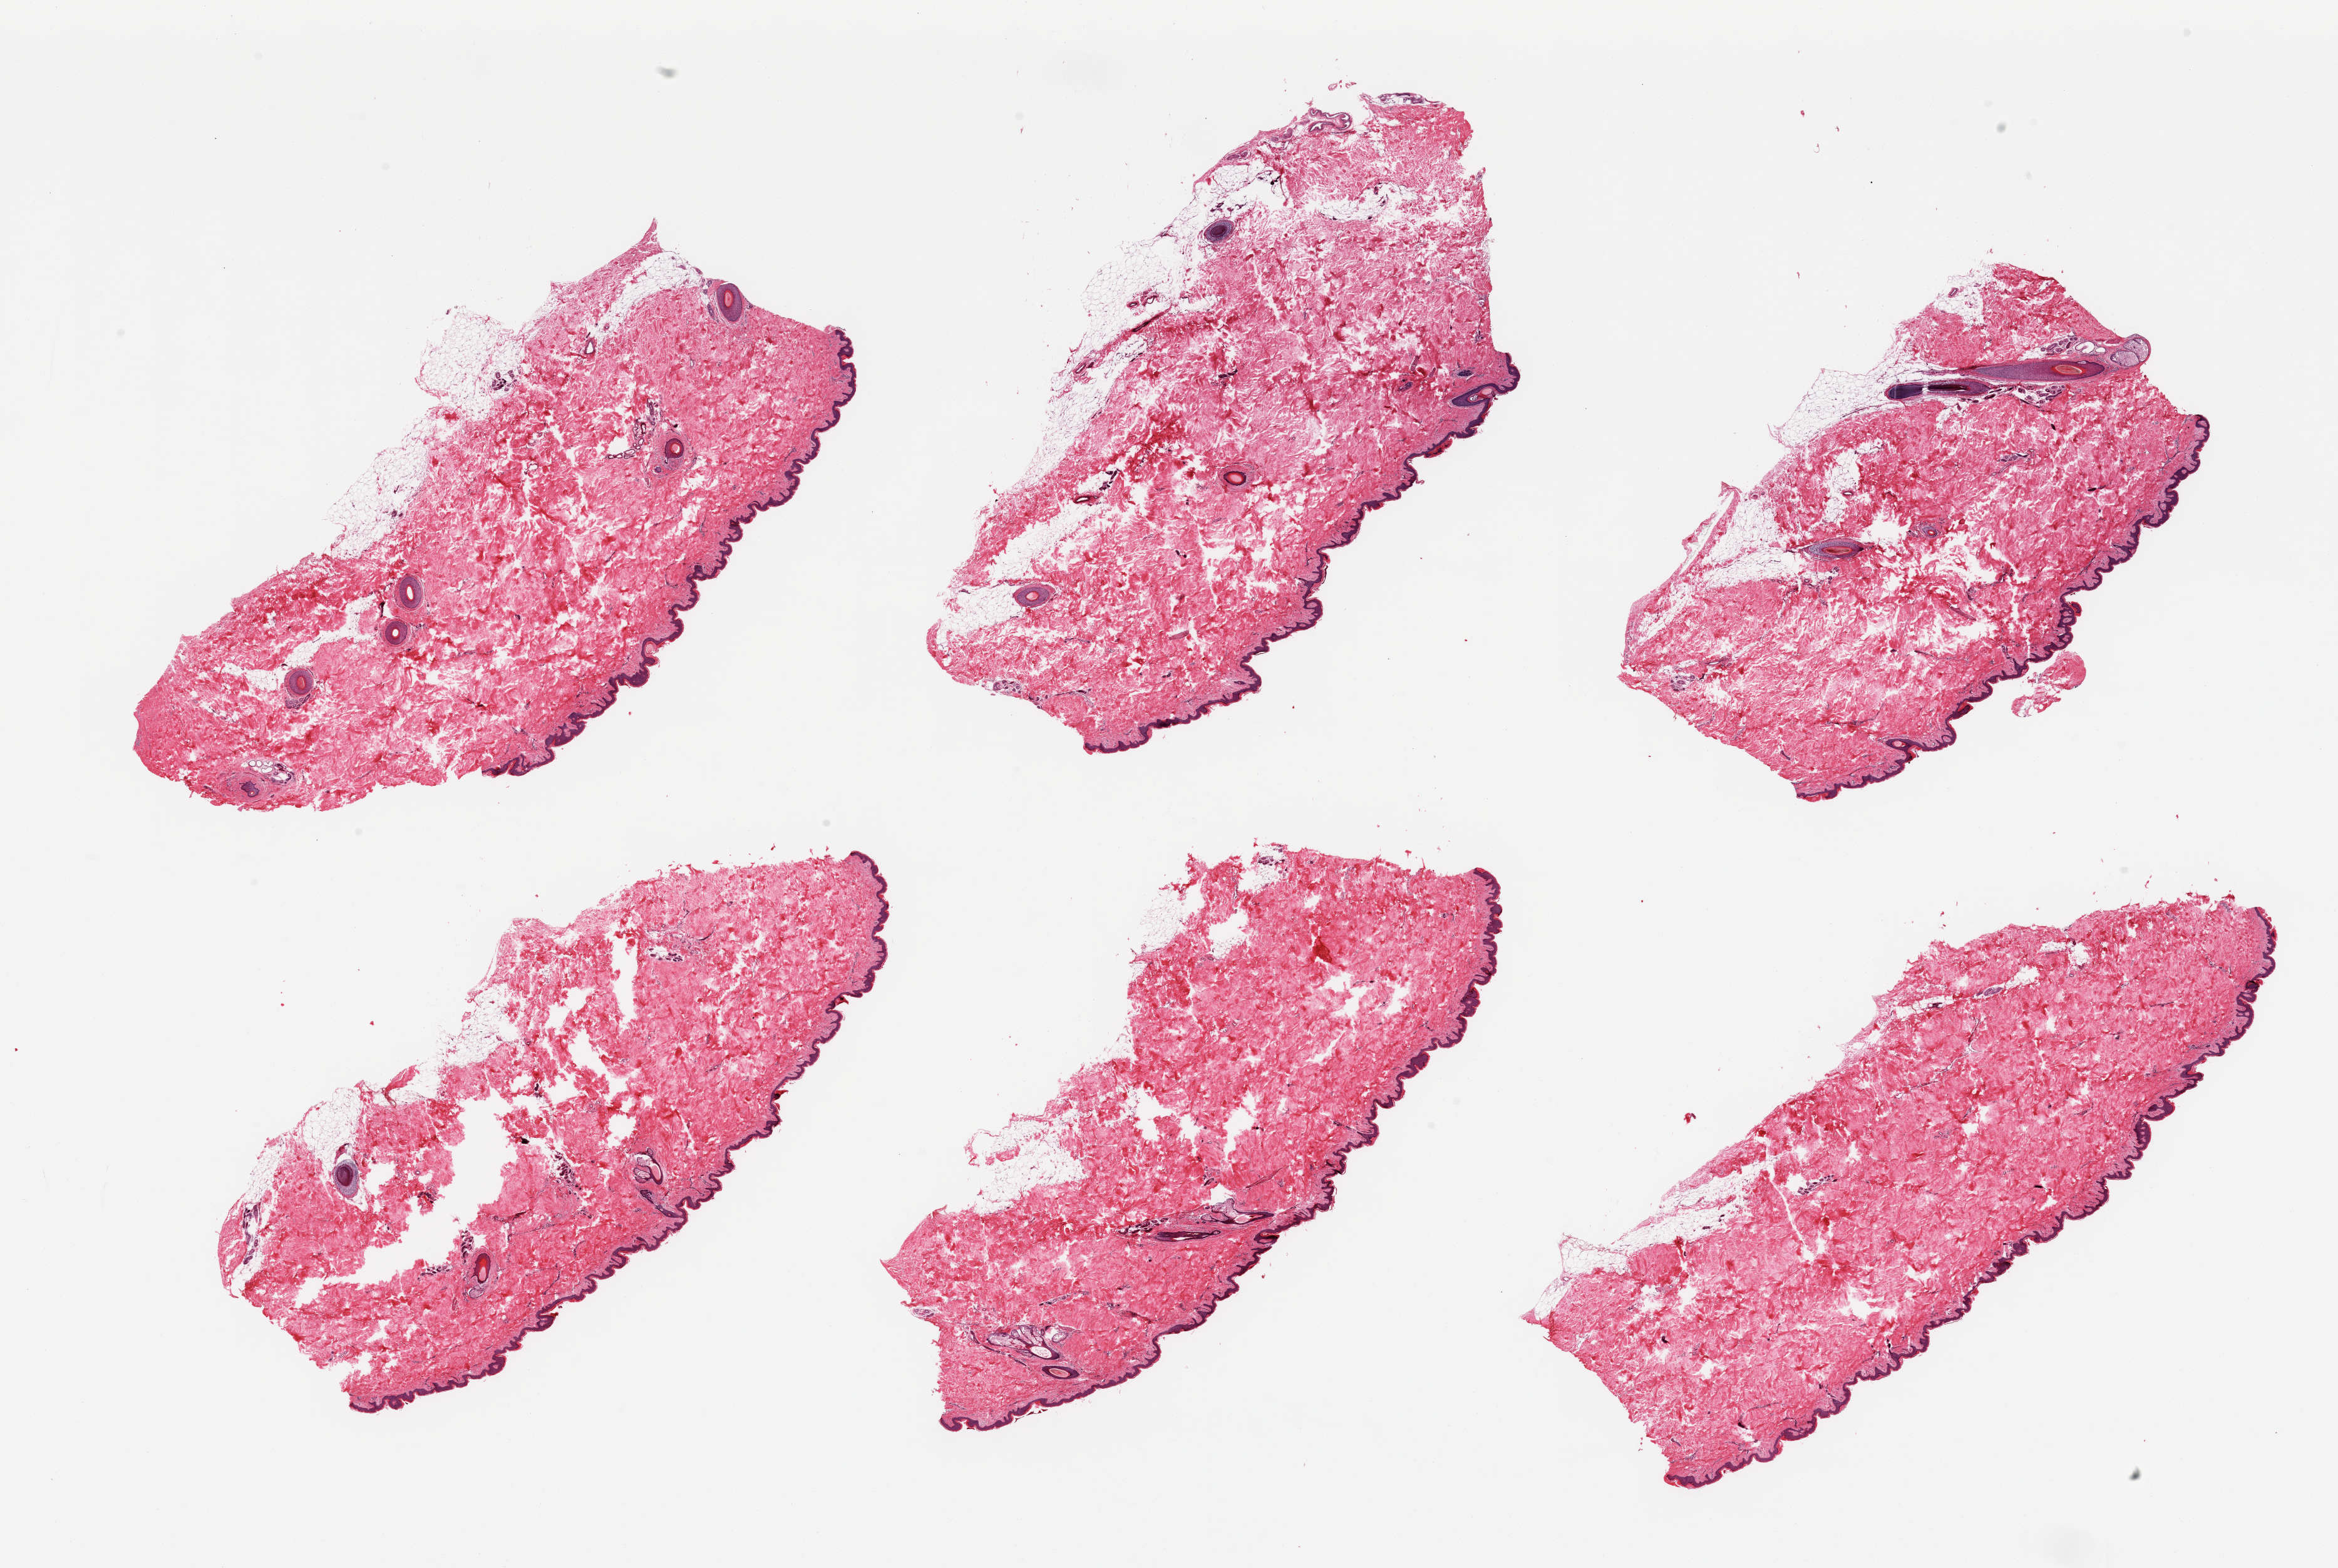
Digitized H&E-stained section, brightfield — whole scanned area (about 29.5 x 19.8 mm, slide scanned at 20x) shown as a low-resolution overview, PAXgene-fixed, paraffin-embedded tissue, target tissue: skin of suprapubic region, donor tissue sample. Donor: male.
* reviewer comment on this tissue sample: 6 pieces; hair bearing skin with ~ 15% of external/internal fat